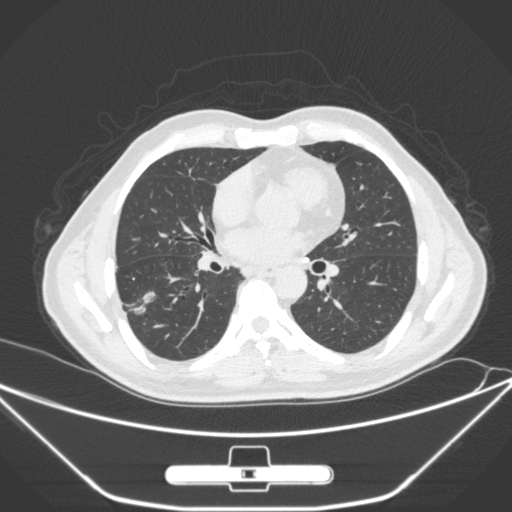
Chest CT, one axial slice. Position 141 of 310 along the scan axis. Lung window (W 1500 / L -600 HU). 512 × 512 image matrix, field of view 398 × 398 mm. Male patient, age 71 years. From the clinical record (not read from this slice): clinical TNM (as recorded): T1c N0 M0.
Structures marked on this image (rectangle marked by the reading radiologist):
- lung tumour (recorded histology: adenocarcinoma): box from (x=126, y=288) to (x=163, y=315) px